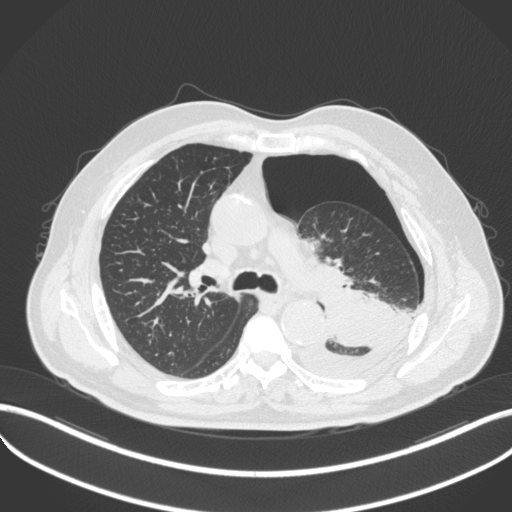
Chest CT, one axial slice; position 334 of 466 along the scan axis; reconstruction kernel B31f; 120 kVp; lung window (W 1500 / L -600 HU); 1 mm slice thickness; 512 × 512 image matrix. Patient: male, 76 years. Case-level facts recorded for this patient, not image findings: clinical TNM (as recorded): T3 N0 M1b.
Outlined on this slice (bounding box drawn by a radiologist):
- lung tumour (recorded histology: adenocarcinoma): bounding box (x1, y1, x2, y2) in pixels: (312, 278, 401, 351)